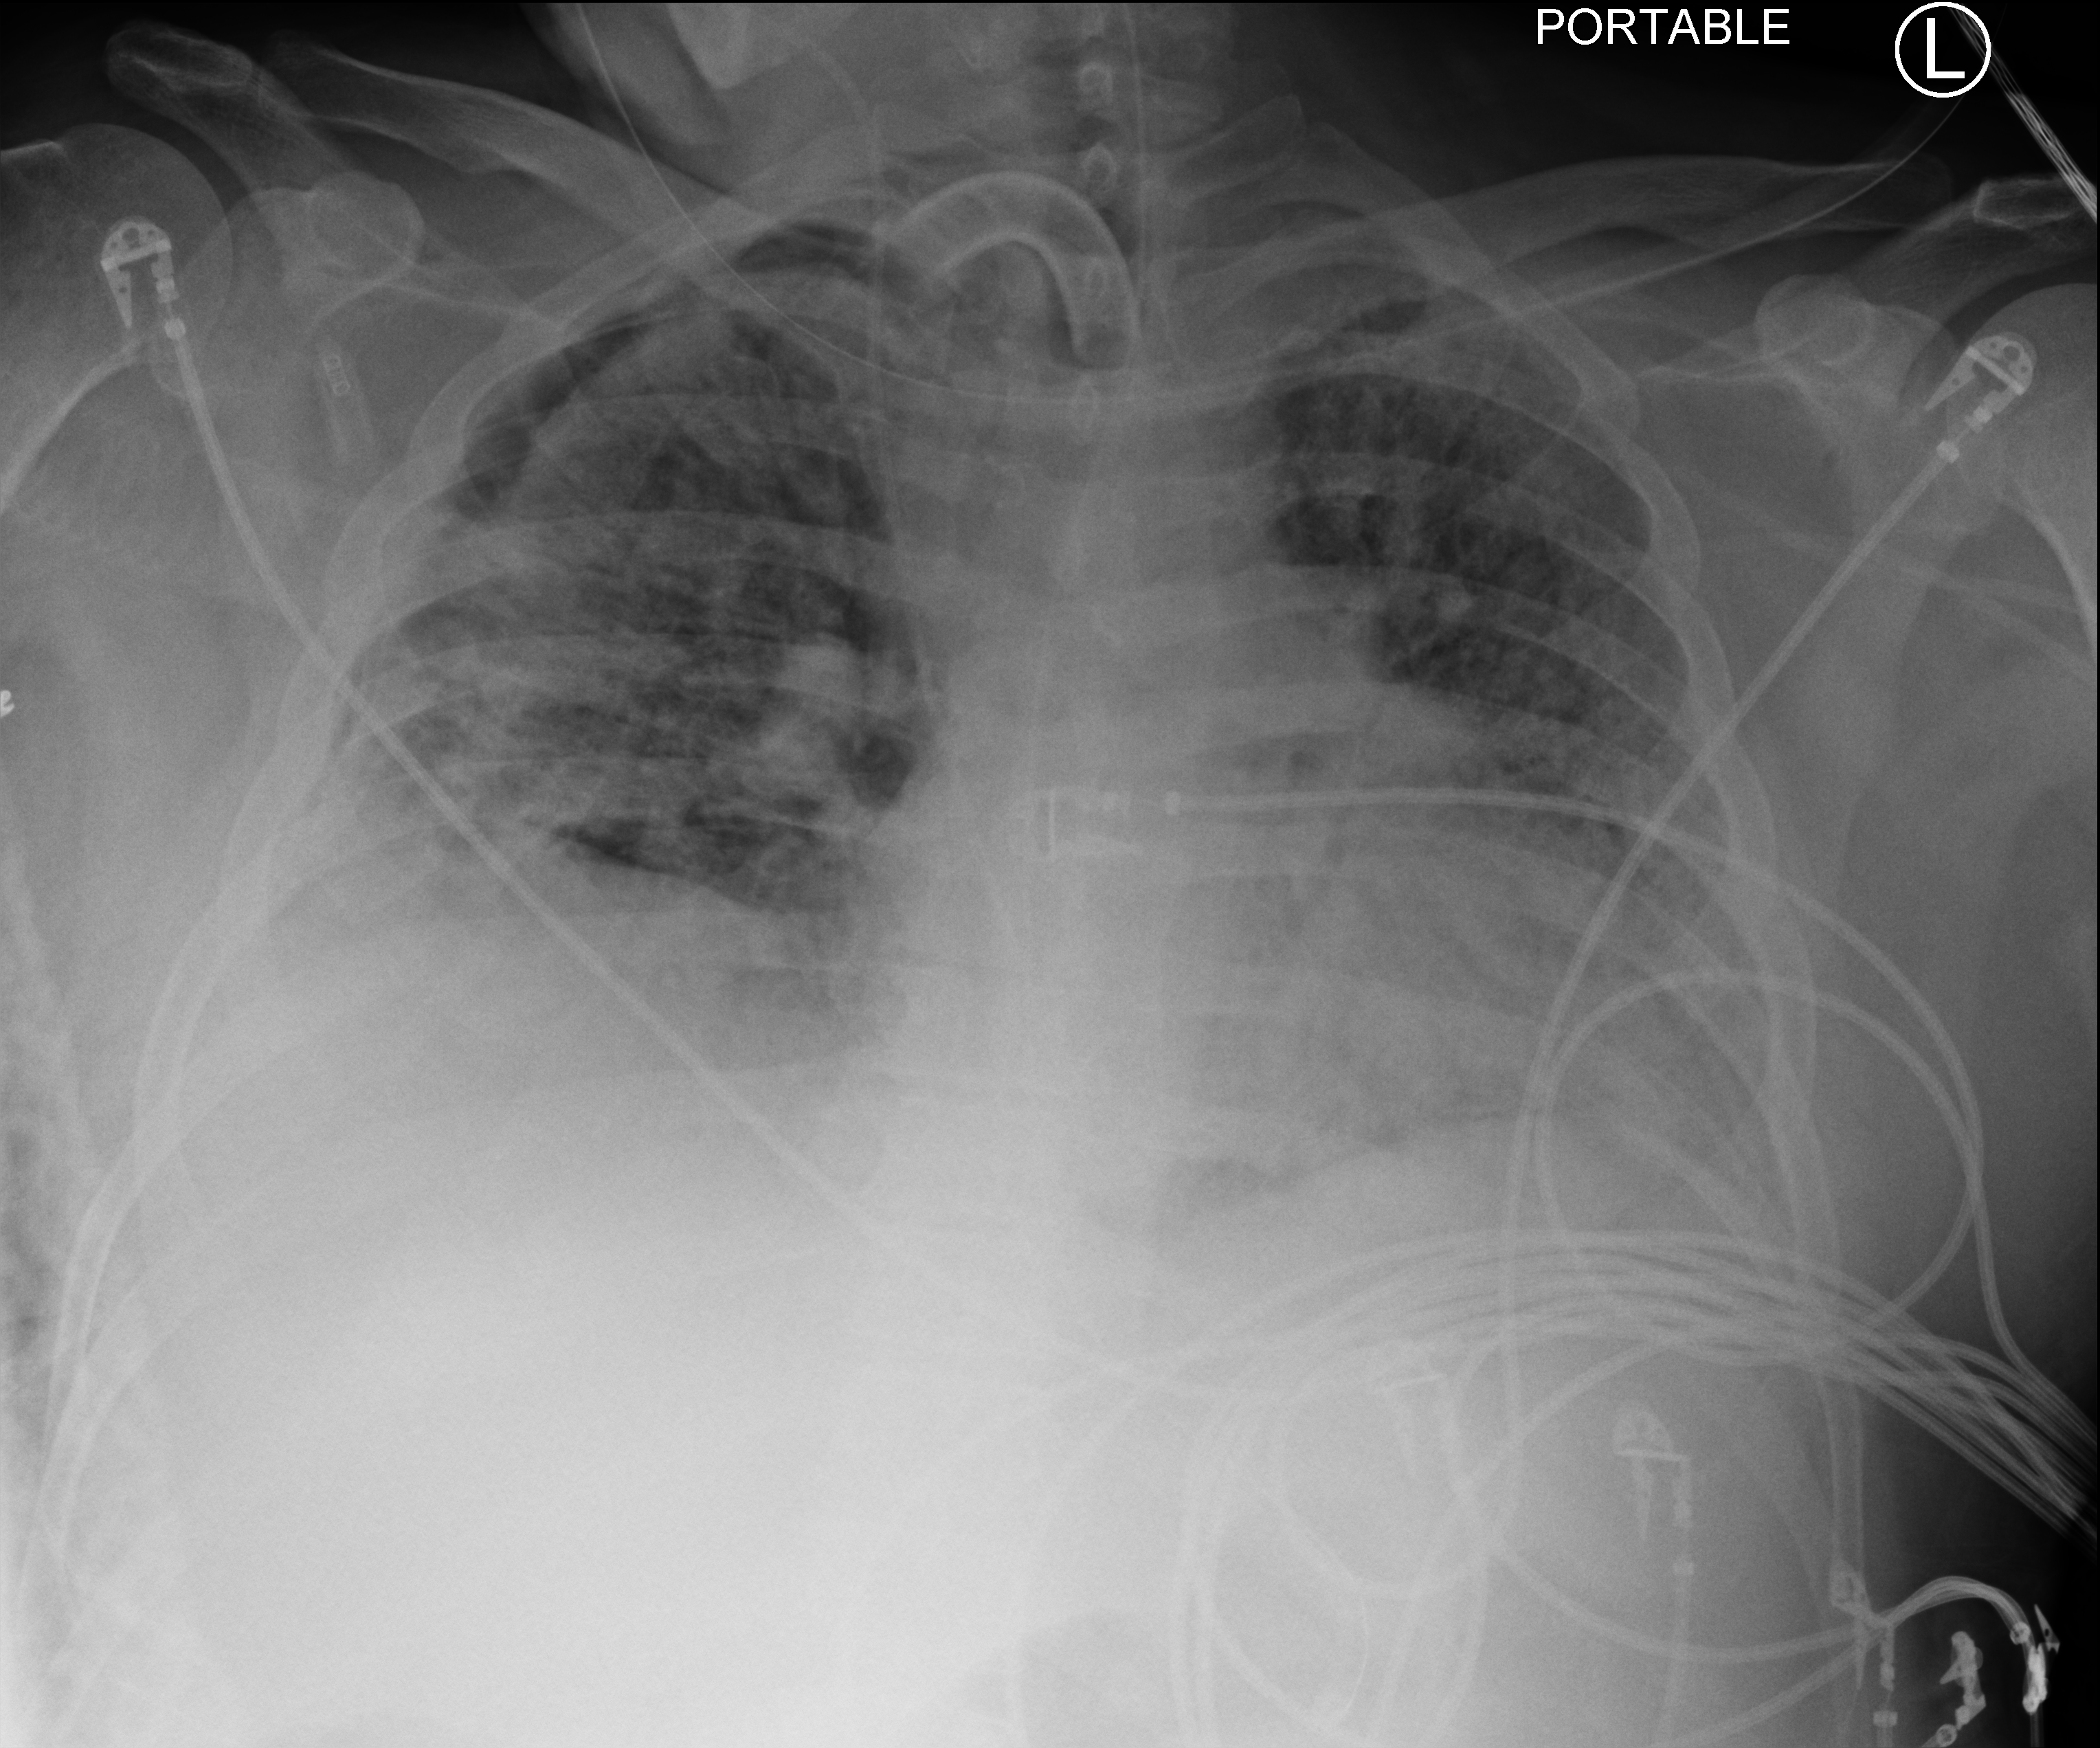
Chest X-ray (portable); anteroposterior (AP) projection. Patient hospitalised with COVID-19; male, aged 18–59 years.
Admission-level facts for this patient (not findings on this image; timing relative to this image not recorded): admitted to intensive care during this hospital stay: yes; chronic kidney disease (admission record): no.